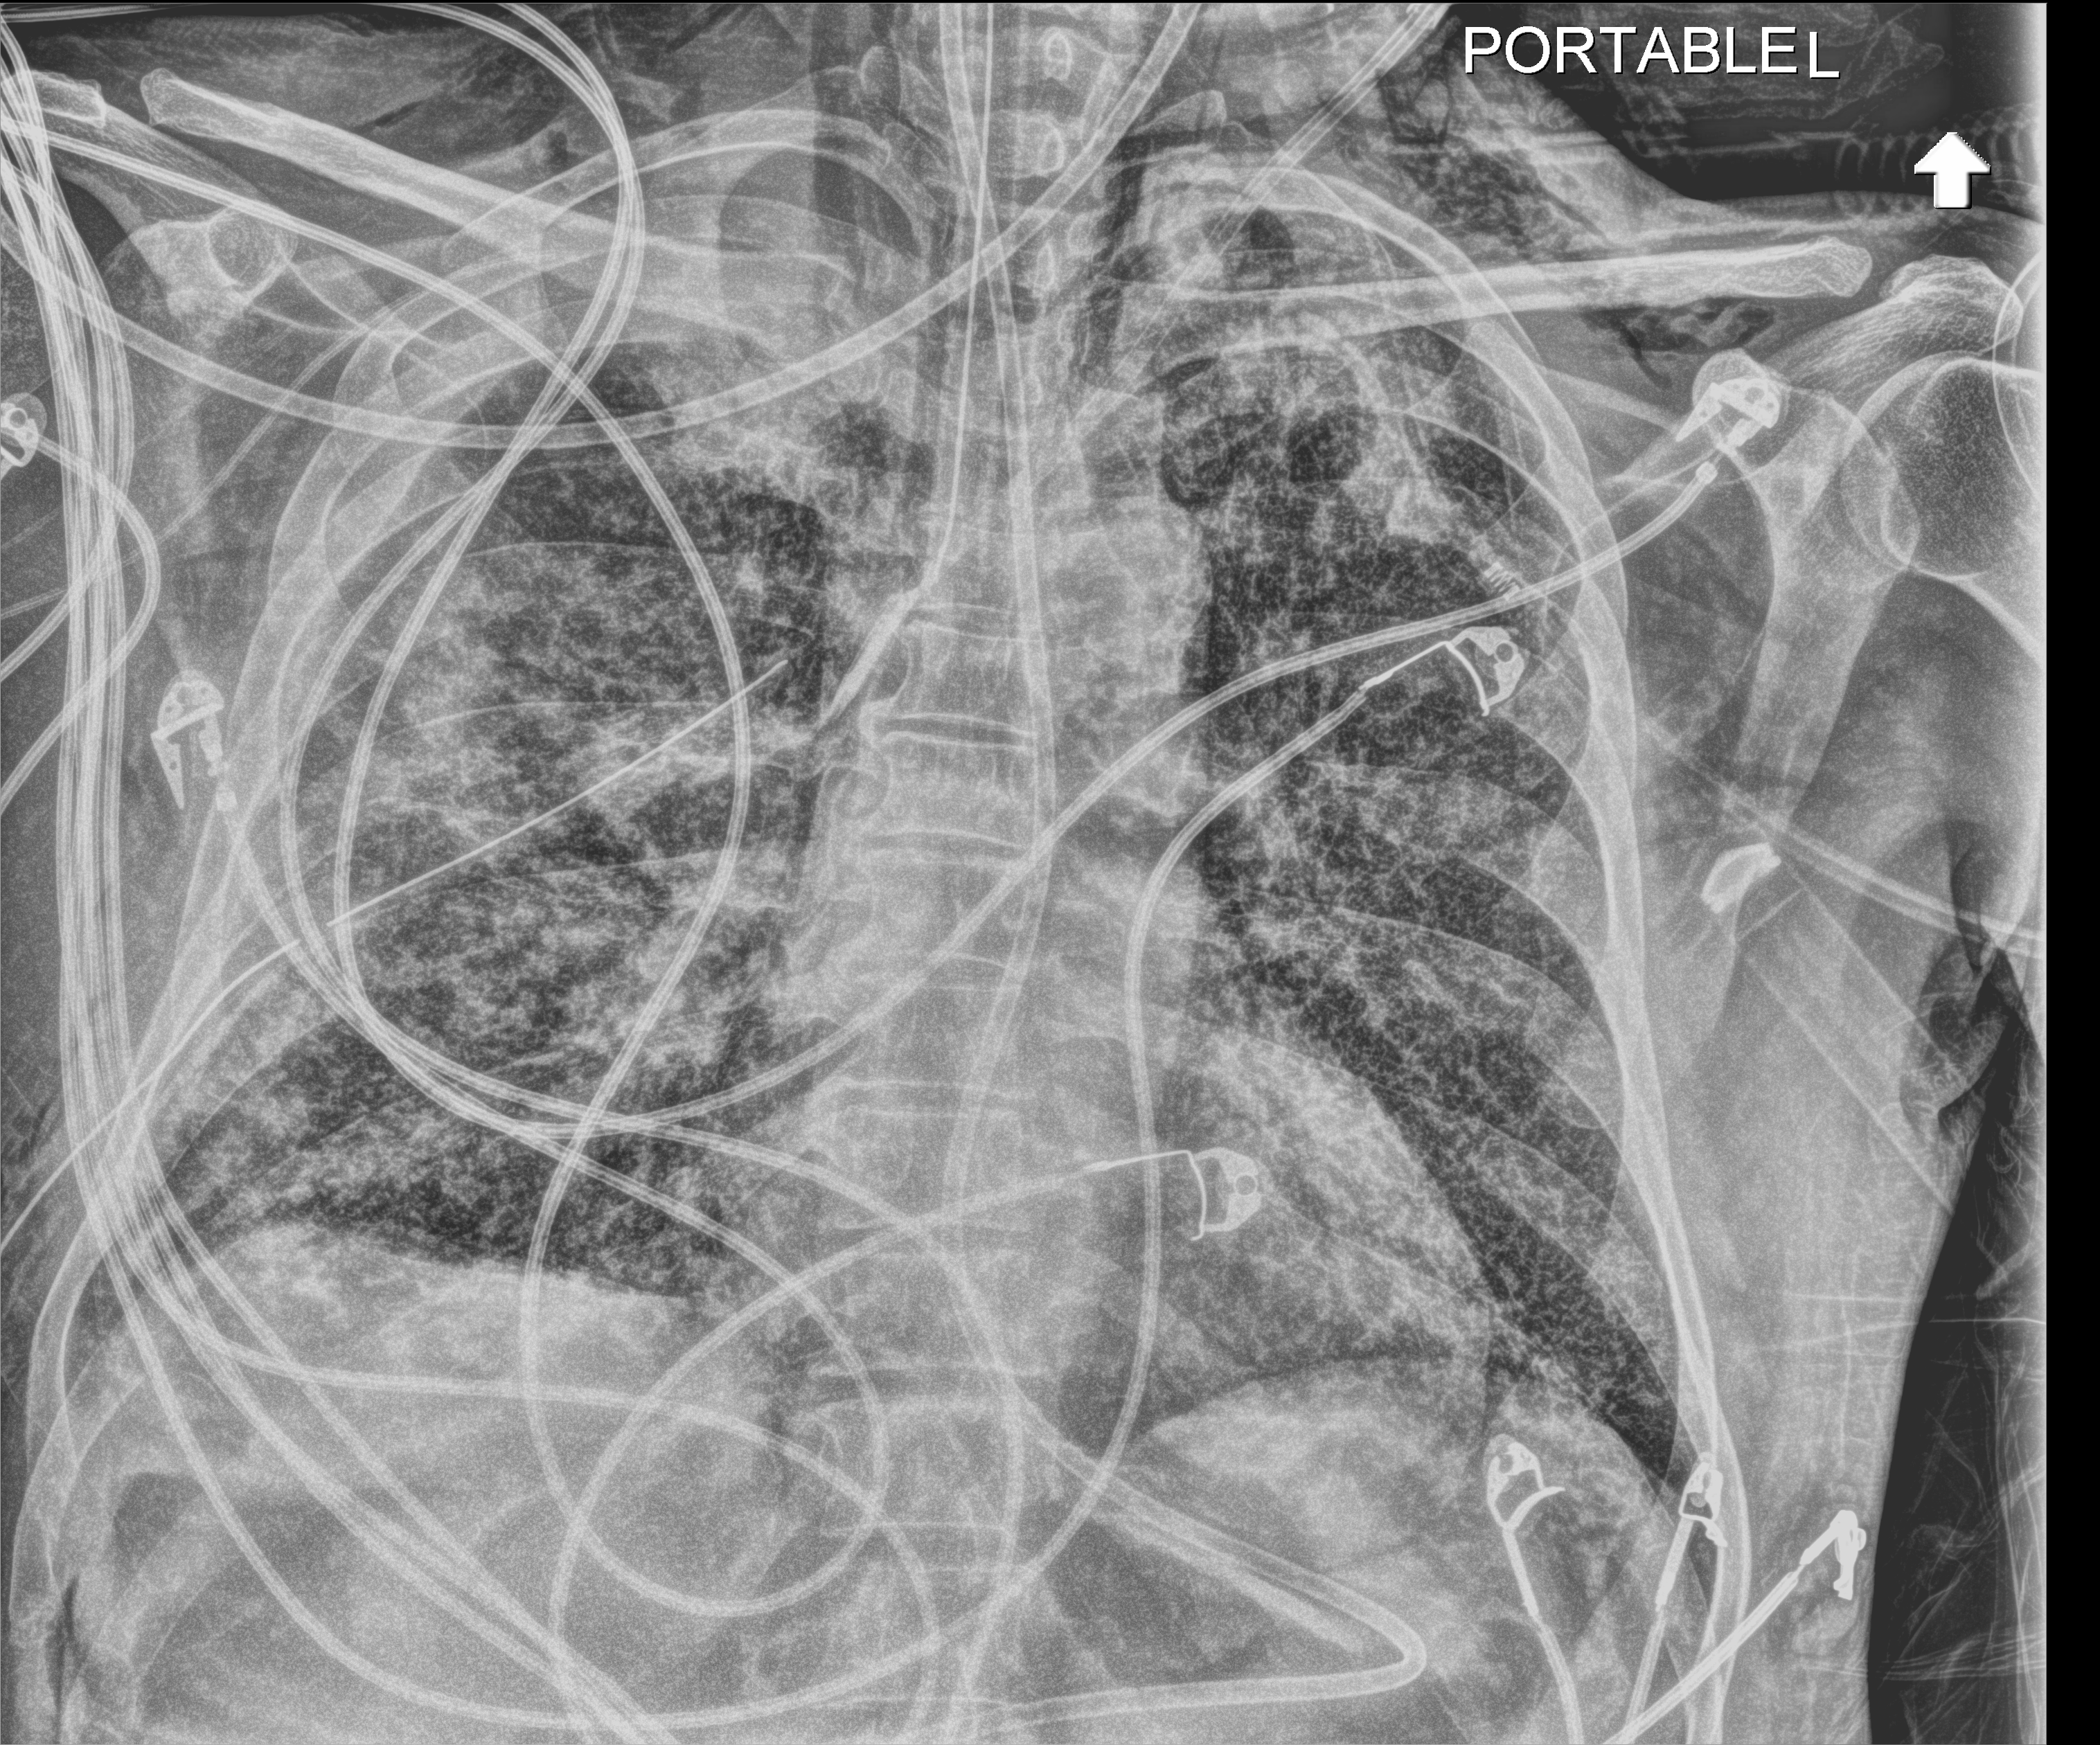
Bedside chest radiograph (digital radiography), anteroposterior (AP) projection. Male patient hospitalised with COVID-19, age 18–59 years.
Admission-level facts for this patient (not findings on this image; timing relative to this image not recorded): other chronic lung disease (admission record): no.